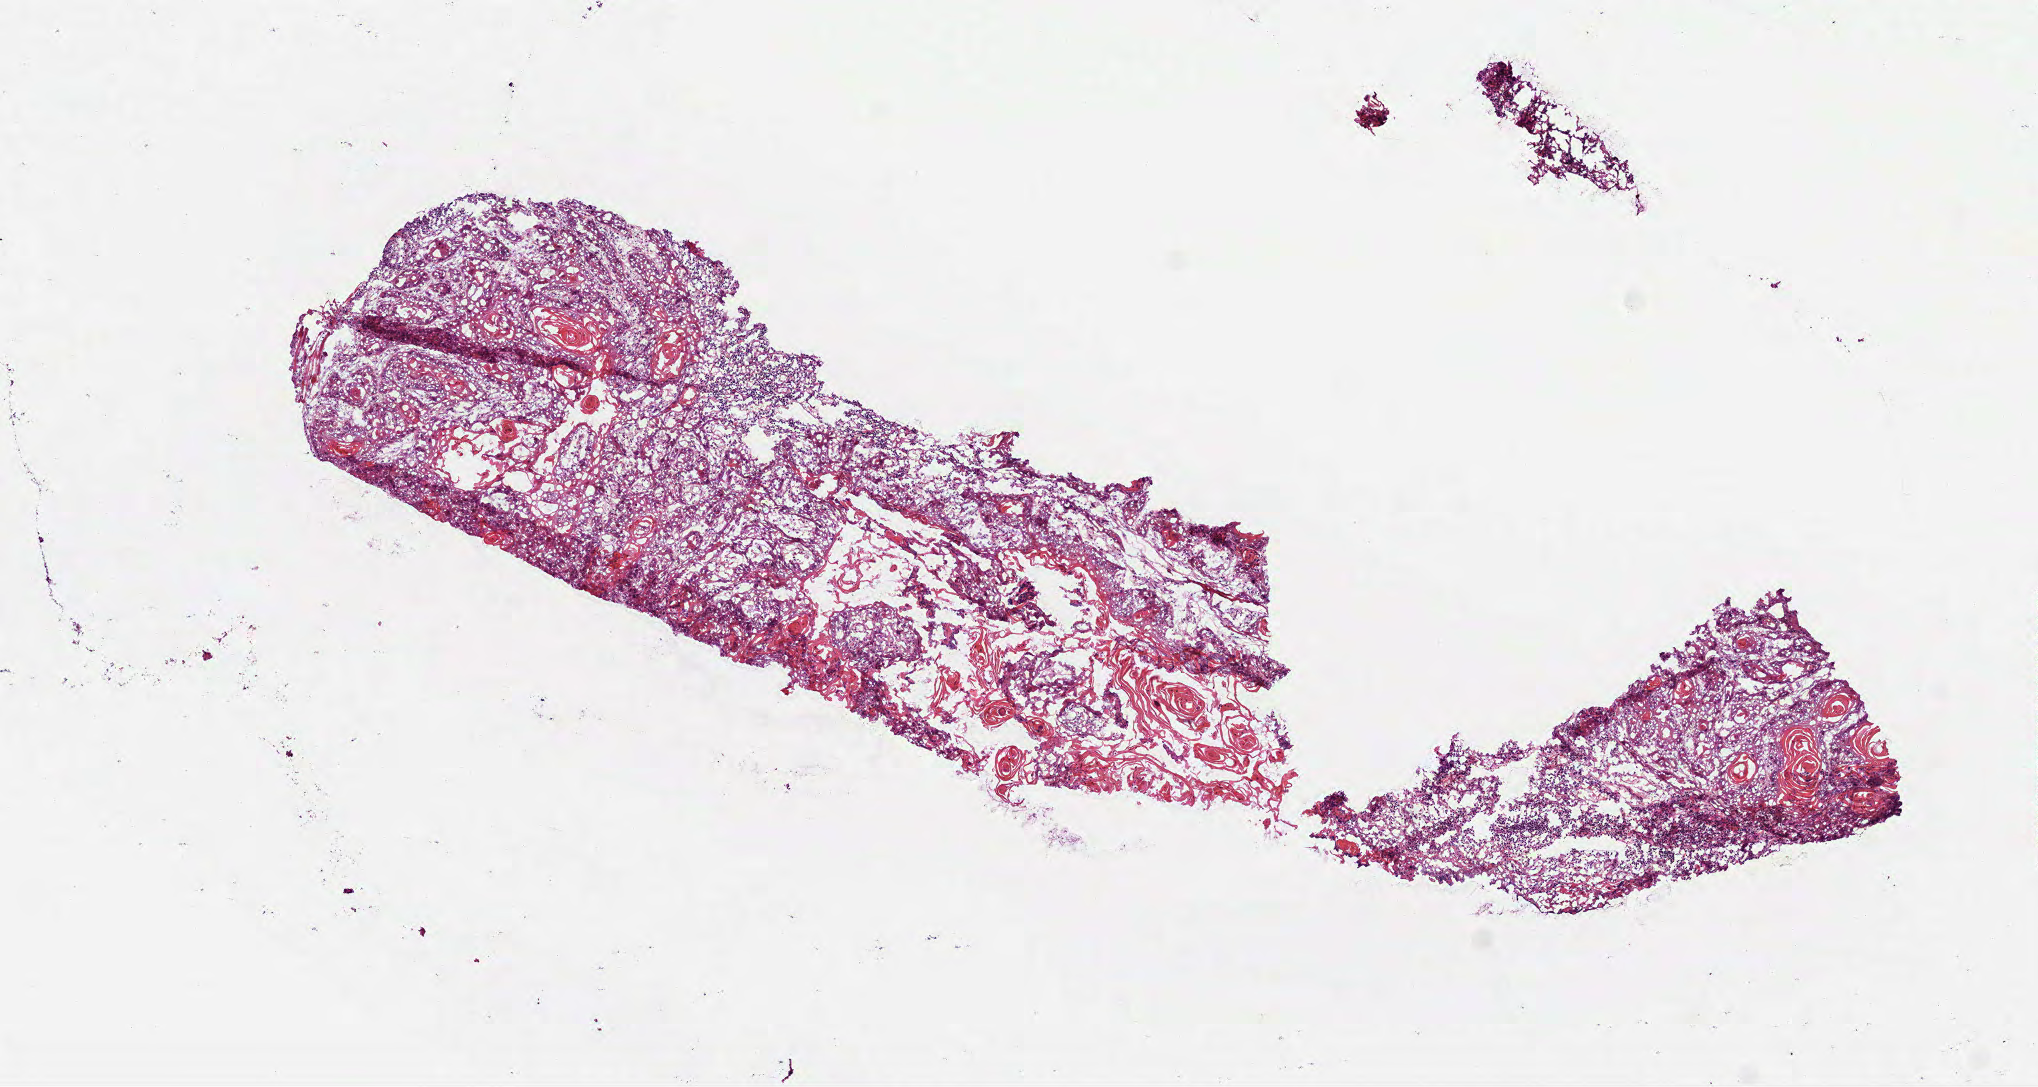
Digitized H&E-stained tissue section (whole slide), a low-resolution overview of the entire scanned area, about 8.2 x 4.4 mm (slide scanned at 40x). Frozen section. Primary tumour sample from the head and neck. Male, age 40 years at initial diagnosis. Histologic grade: G2 (moderately differentiated). Composition of this section per pathologist review: tumour cells 100%, tumour nuclei 55%, normal cells 0%, stromal cells 0%, necrosis 0%. Inflammatory infiltration, as recorded: lymphocyte infiltration 40%, monocyte infiltration 0%, neutrophil infiltration 2%.
AJCC pathologic stage: II. Histologic diagnosis: Squamous cell carcinoma, NOS (tongue, NOS).